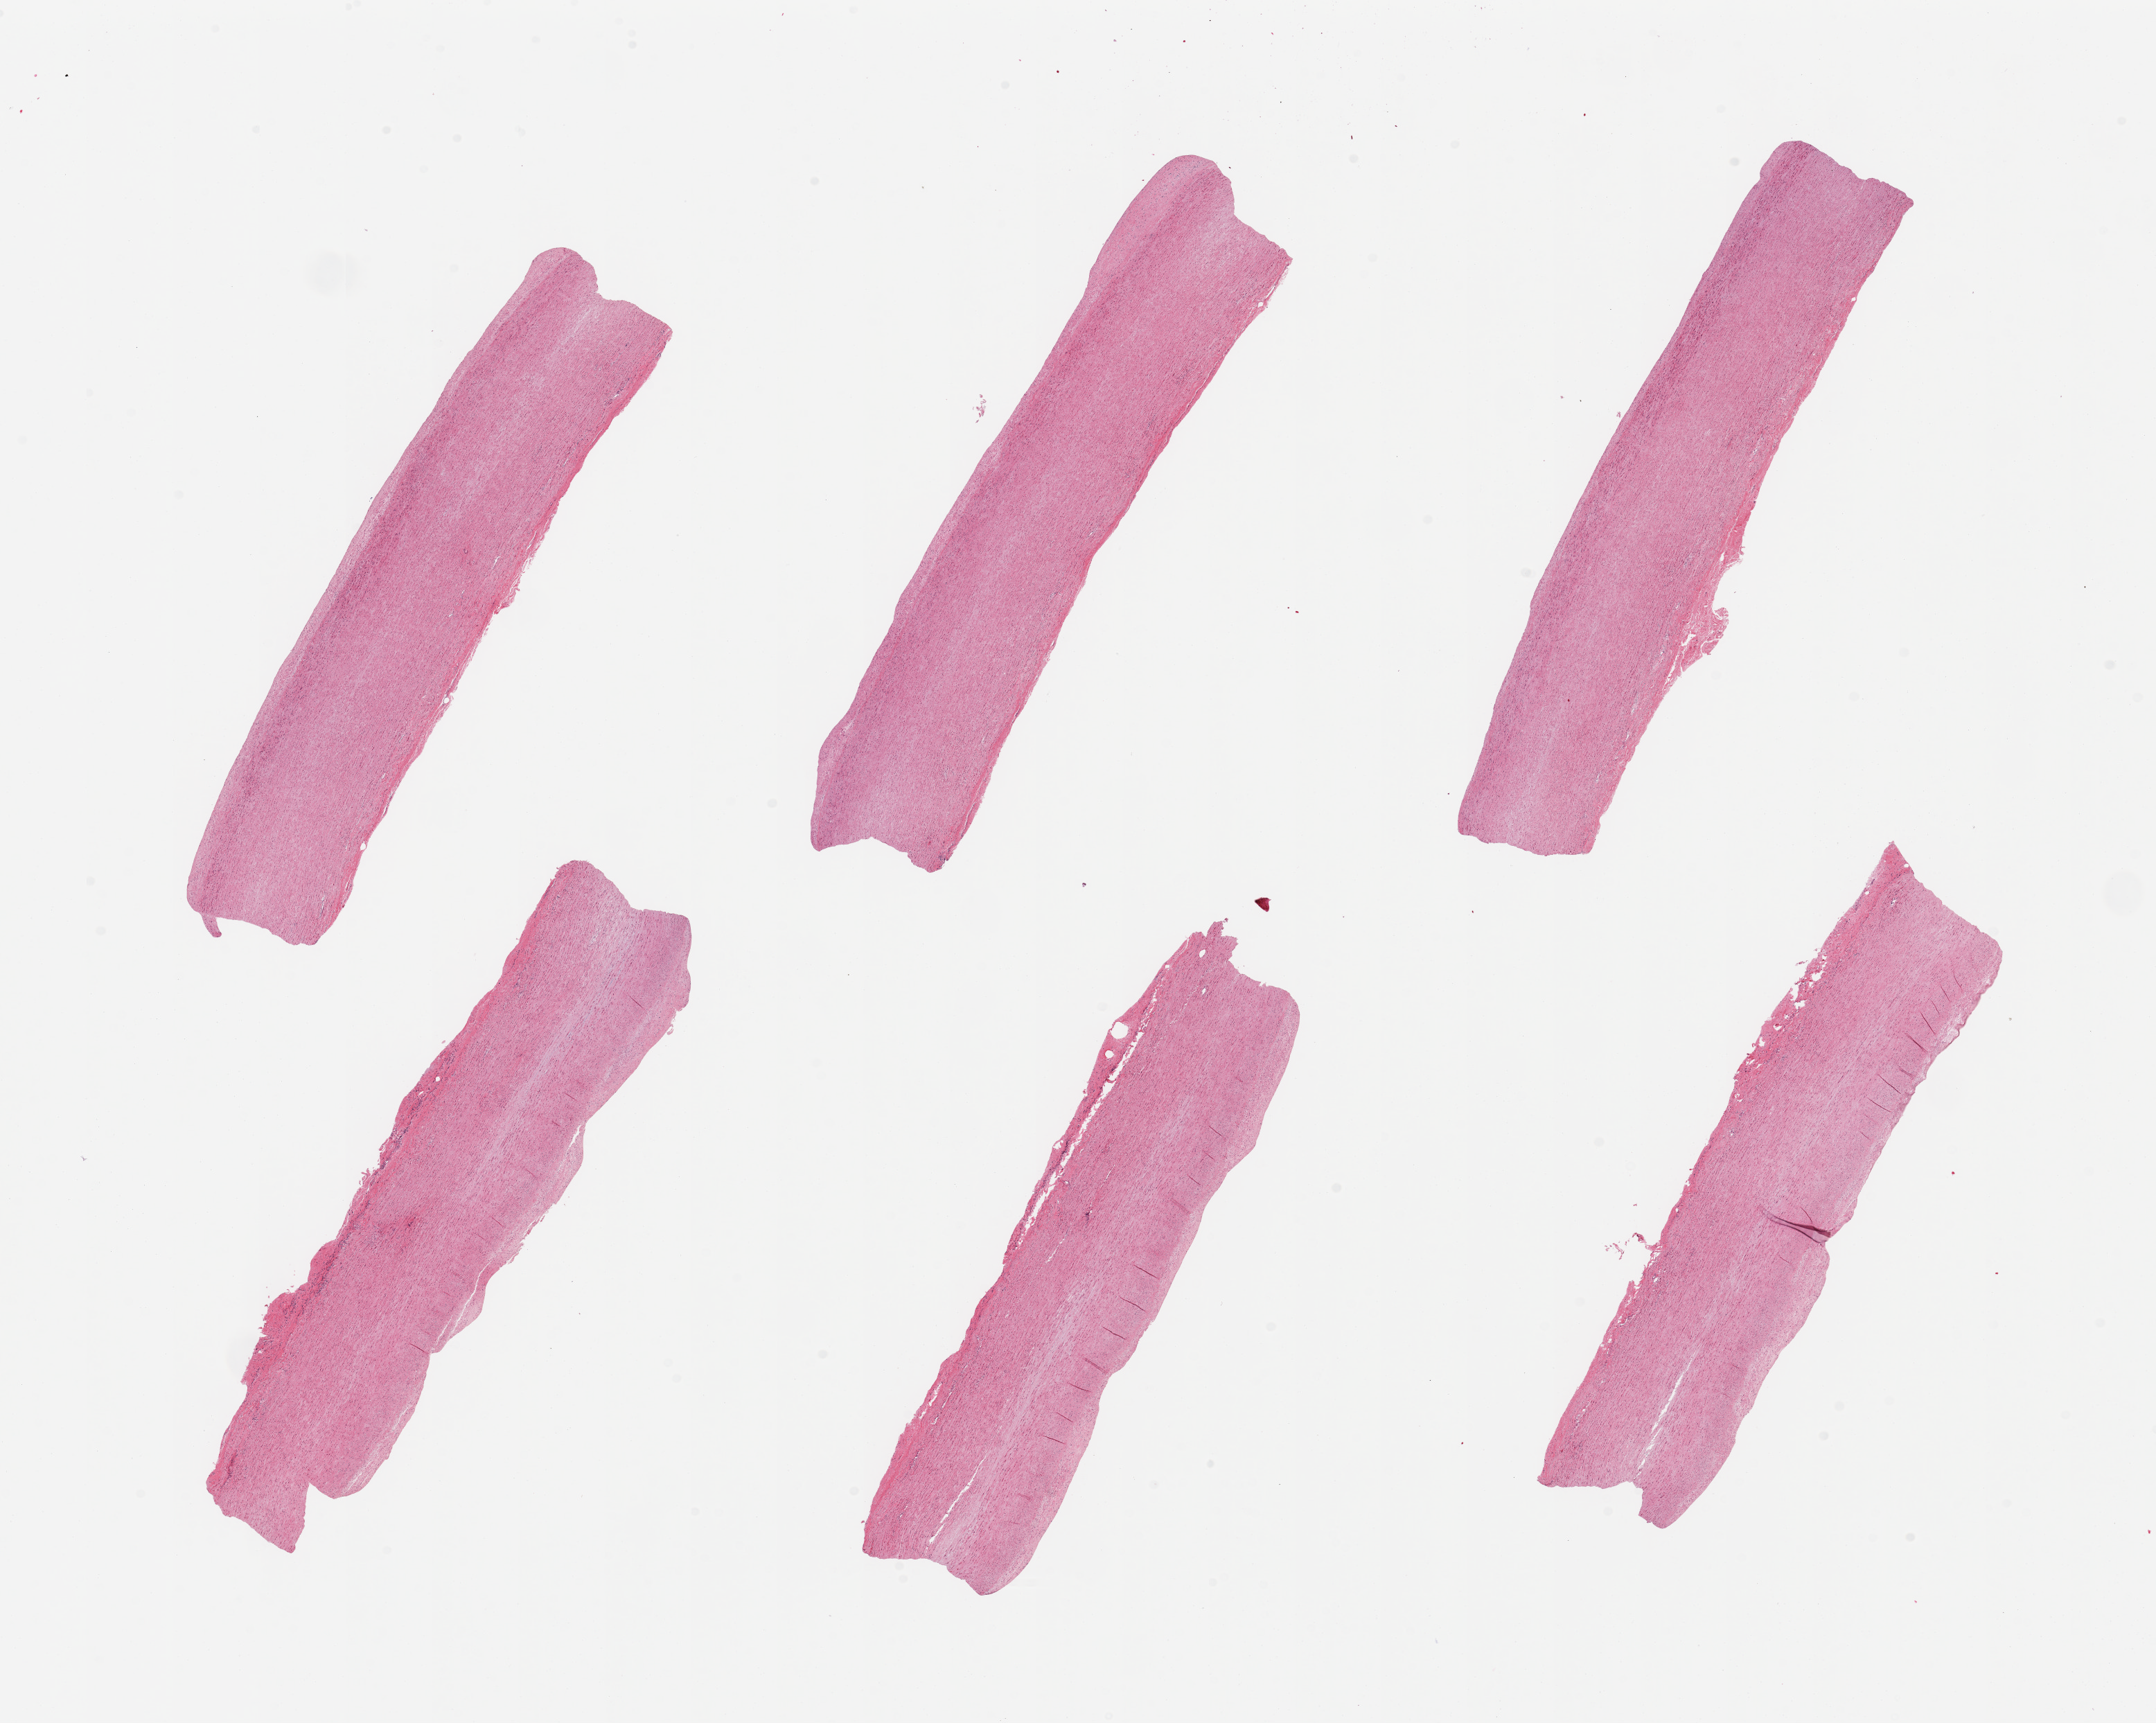
Hematoxylin and eosin (H&E) whole-slide image, low-resolution overview of the scanned area, about 24.6 x 19.7 mm; PAXgene-fixed paraffin-embedded (PFPE) section; target tissue: aorta; donor tissue sample. Donor: male.
* pathologist's review note for this sample: 6 pieces, atherosis up to ~0.3mm